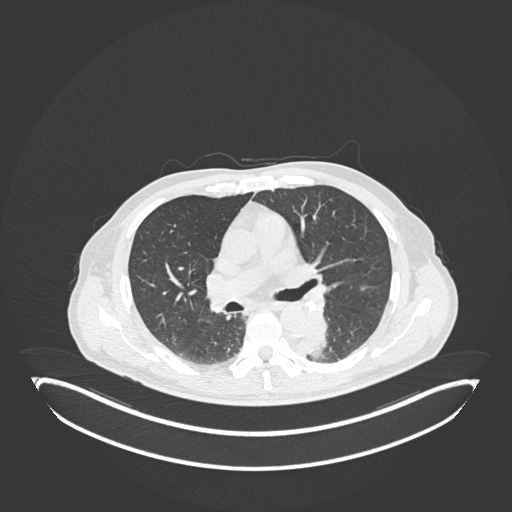
Chest CT, one axial slice; slice 120 of 251 in the series (ordered by position); reconstruction kernel B30f; 120 kVp; lung window (W 1500 / L -600 HU); 512 × 512 image matrix, field of view 500 × 500 mm. Male patient, age 72 years. From the clinical record (not read from this slice): clinical TNM (as recorded): T2b N0 M1.
Annotated regions visible in this slice (bounding box drawn by a radiologist):
- lung tumour (recorded histology: adenocarcinoma): bounding box [x1, y1, x2, y2] px = [299, 313, 330, 359]